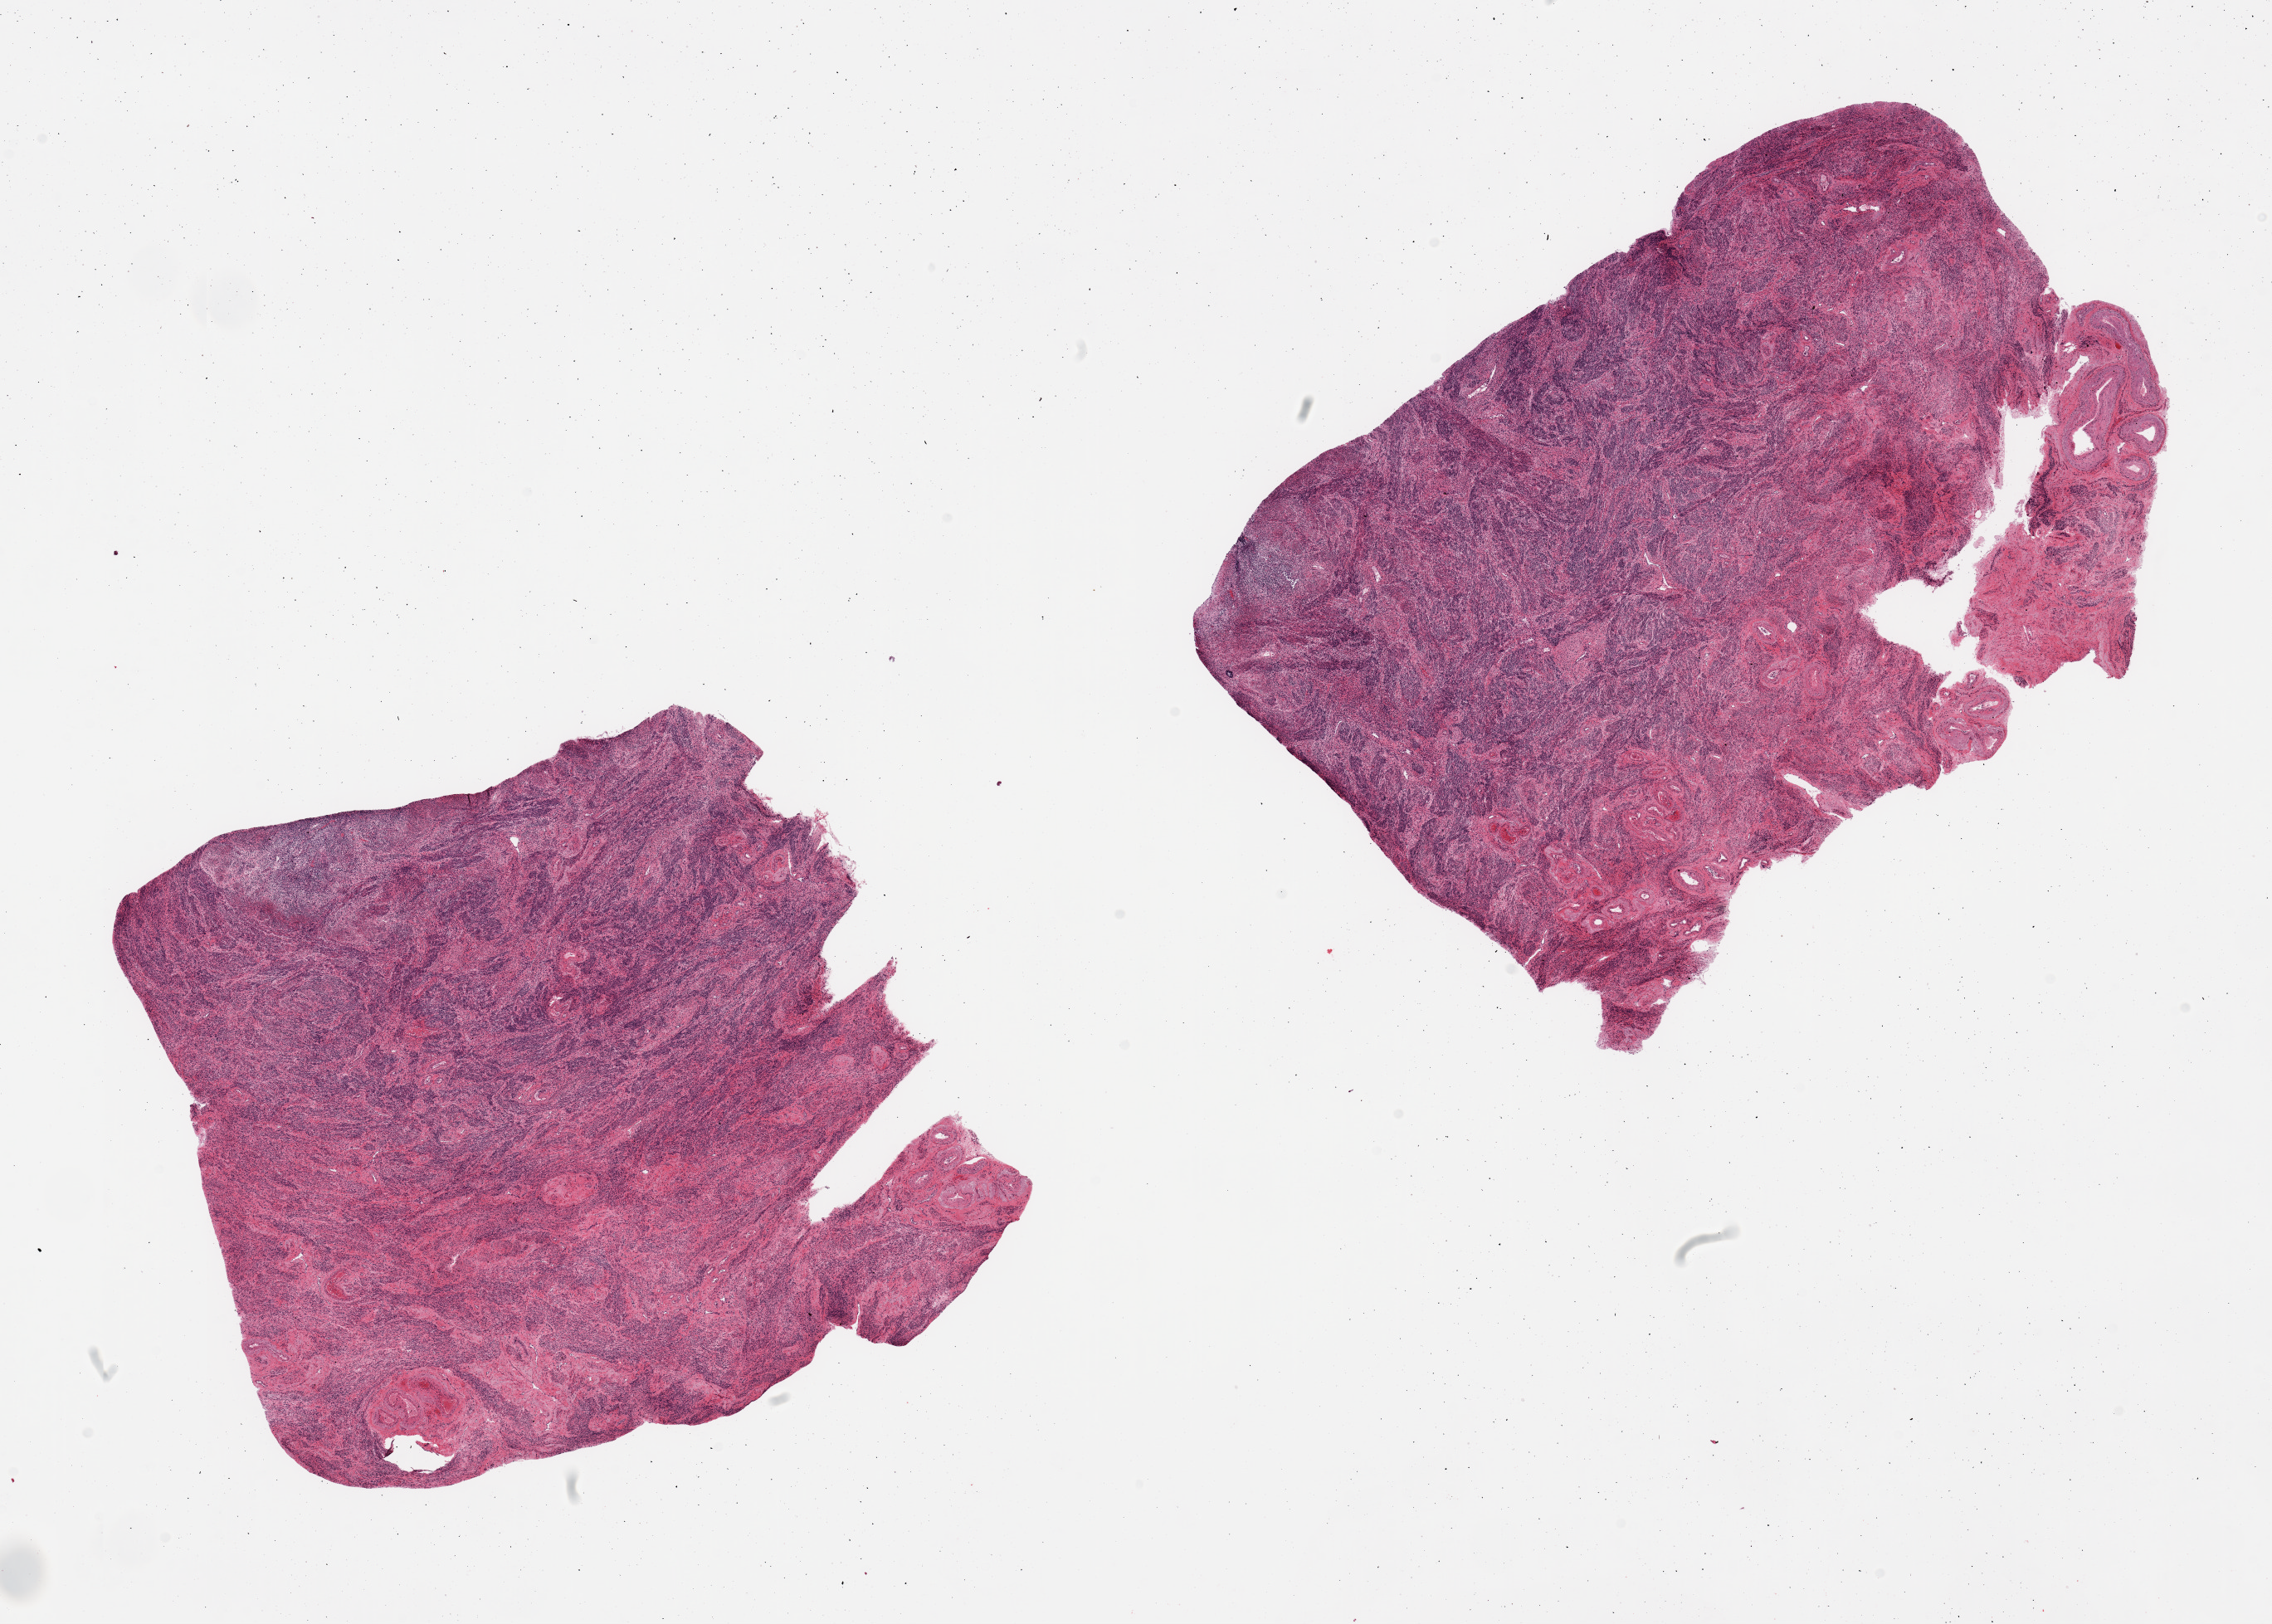
Hematoxylin and eosin (H&E) whole-slide image — whole scanned area (about 21.7 x 15.5 mm, from a 20x scan) shown as a low-resolution overview. PAXgene-fixed paraffin-embedded (PFPE) section. Target tissue: uterus. Tissue donor sample. Female donor.
Review note (as recorded): 2 pieces; only myometrium on this cut.